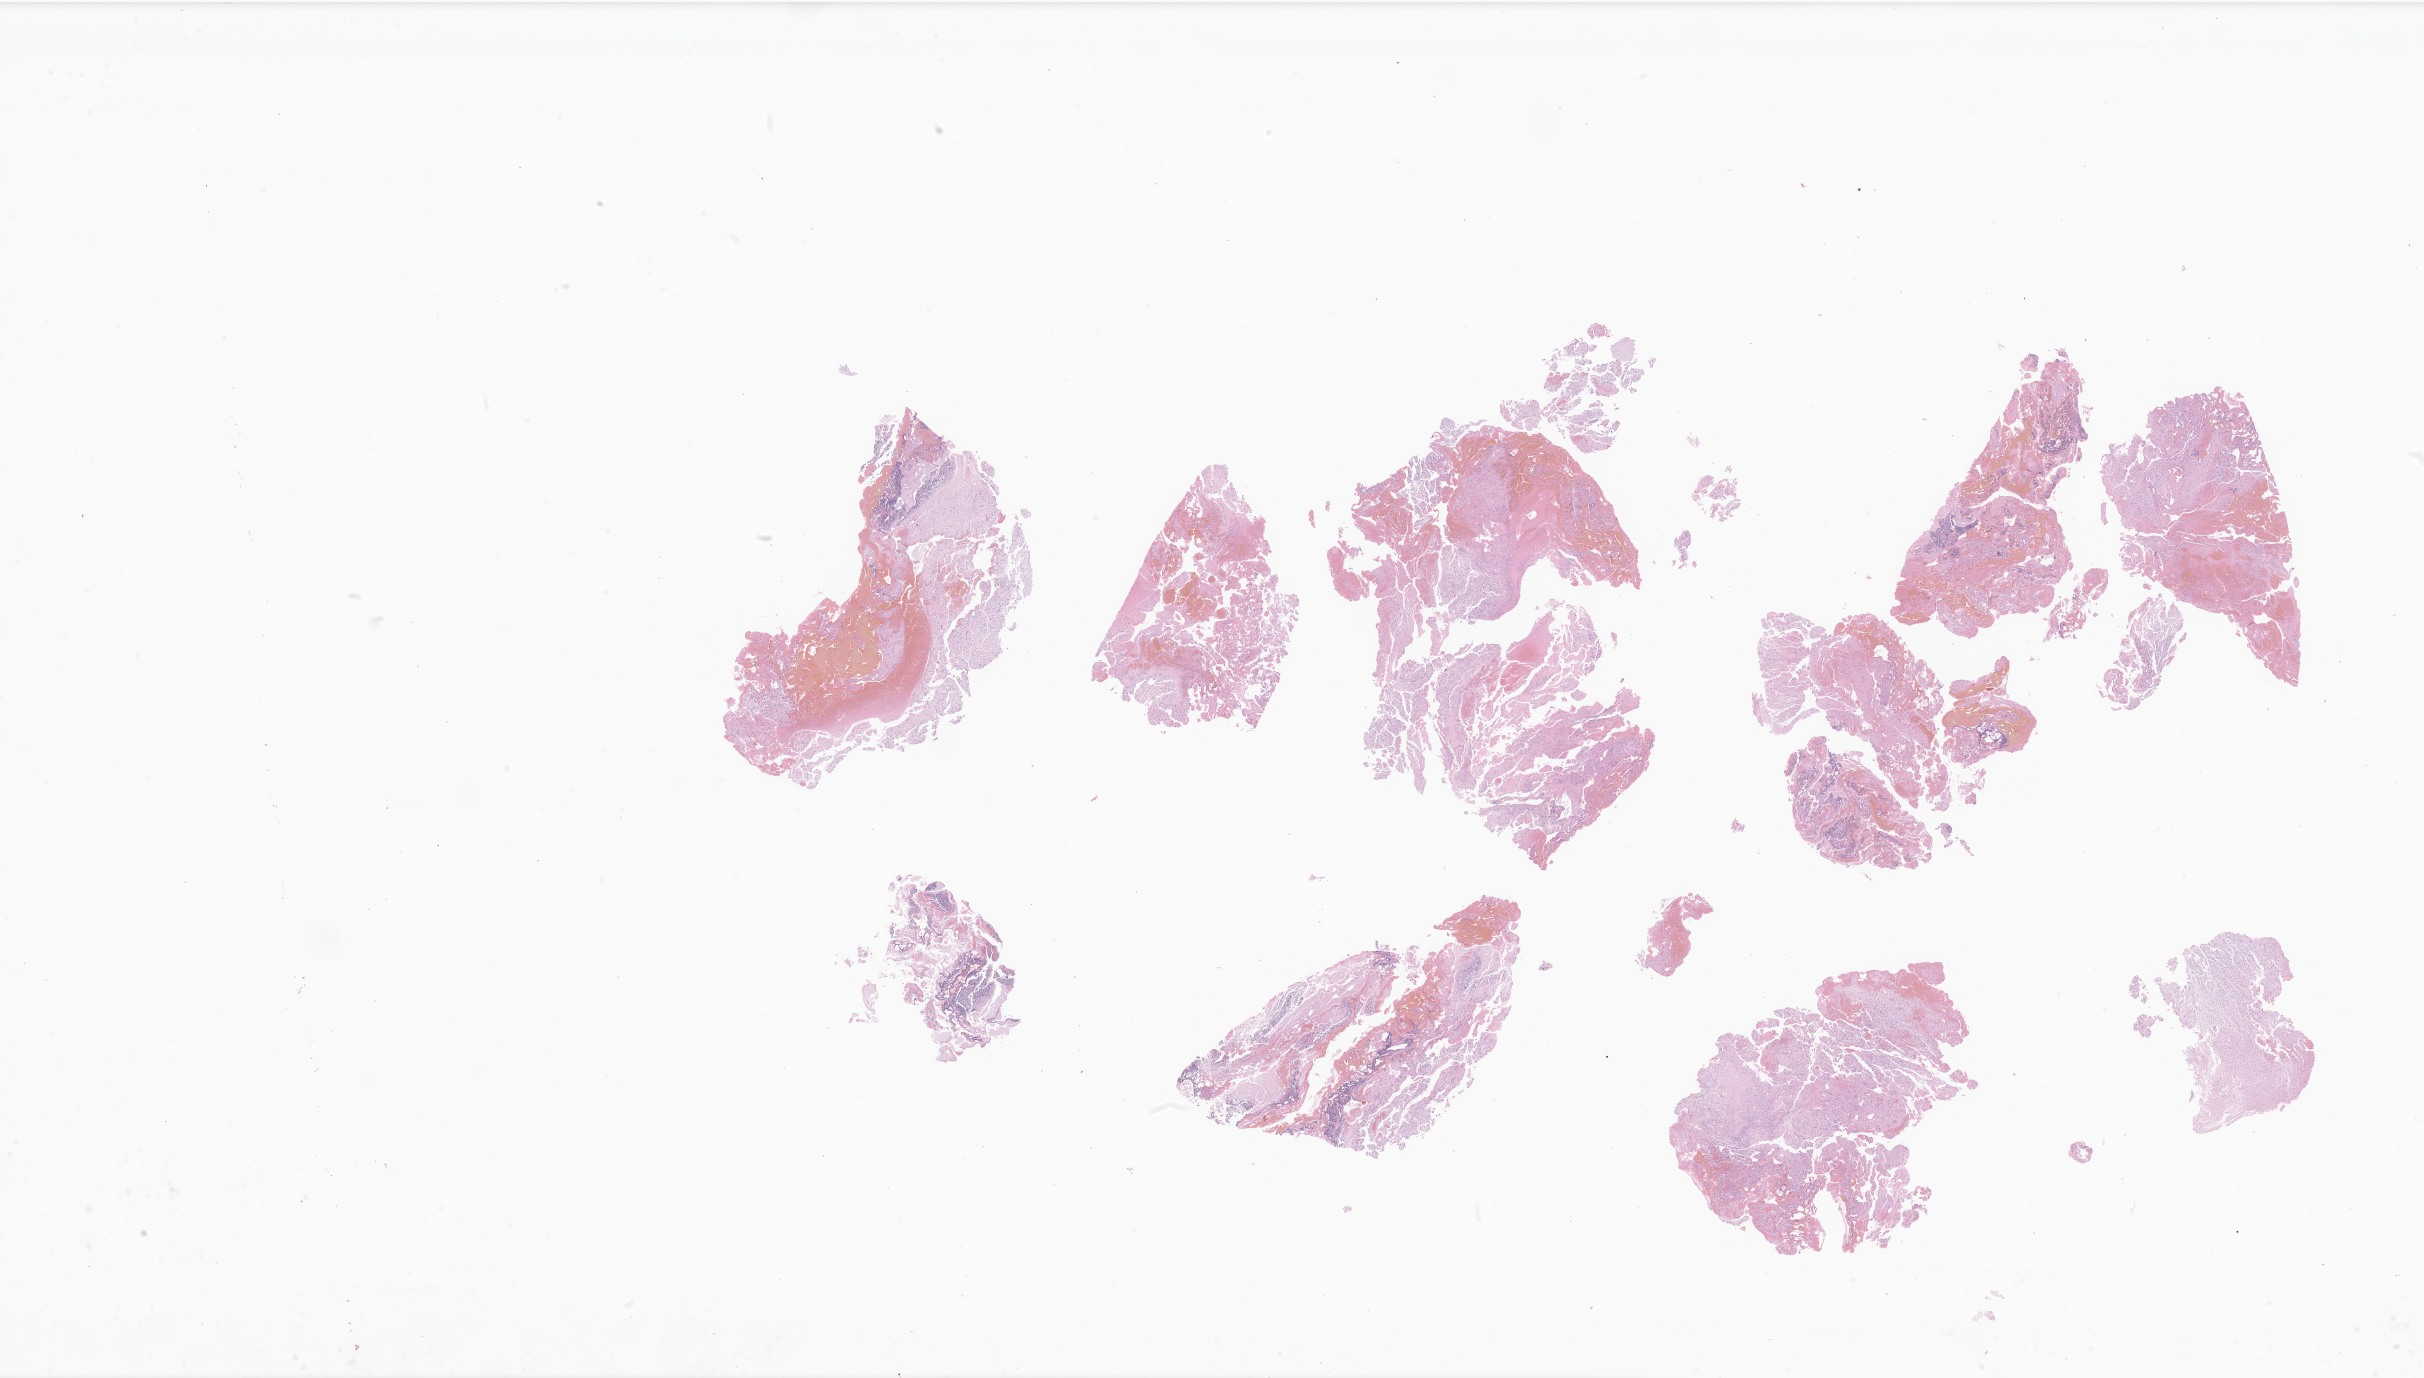
Whole-slide image, H&E stain of tumor tissue from the brain — shown as a low-resolution overview of the whole scanned area (about 40.9 x 23.2 mm). Formalin-fixed paraffin-embedded section. Patient: female, age 308 months (25 years 8 months).
Recorded diagnosis: Neoplasm, malignant.